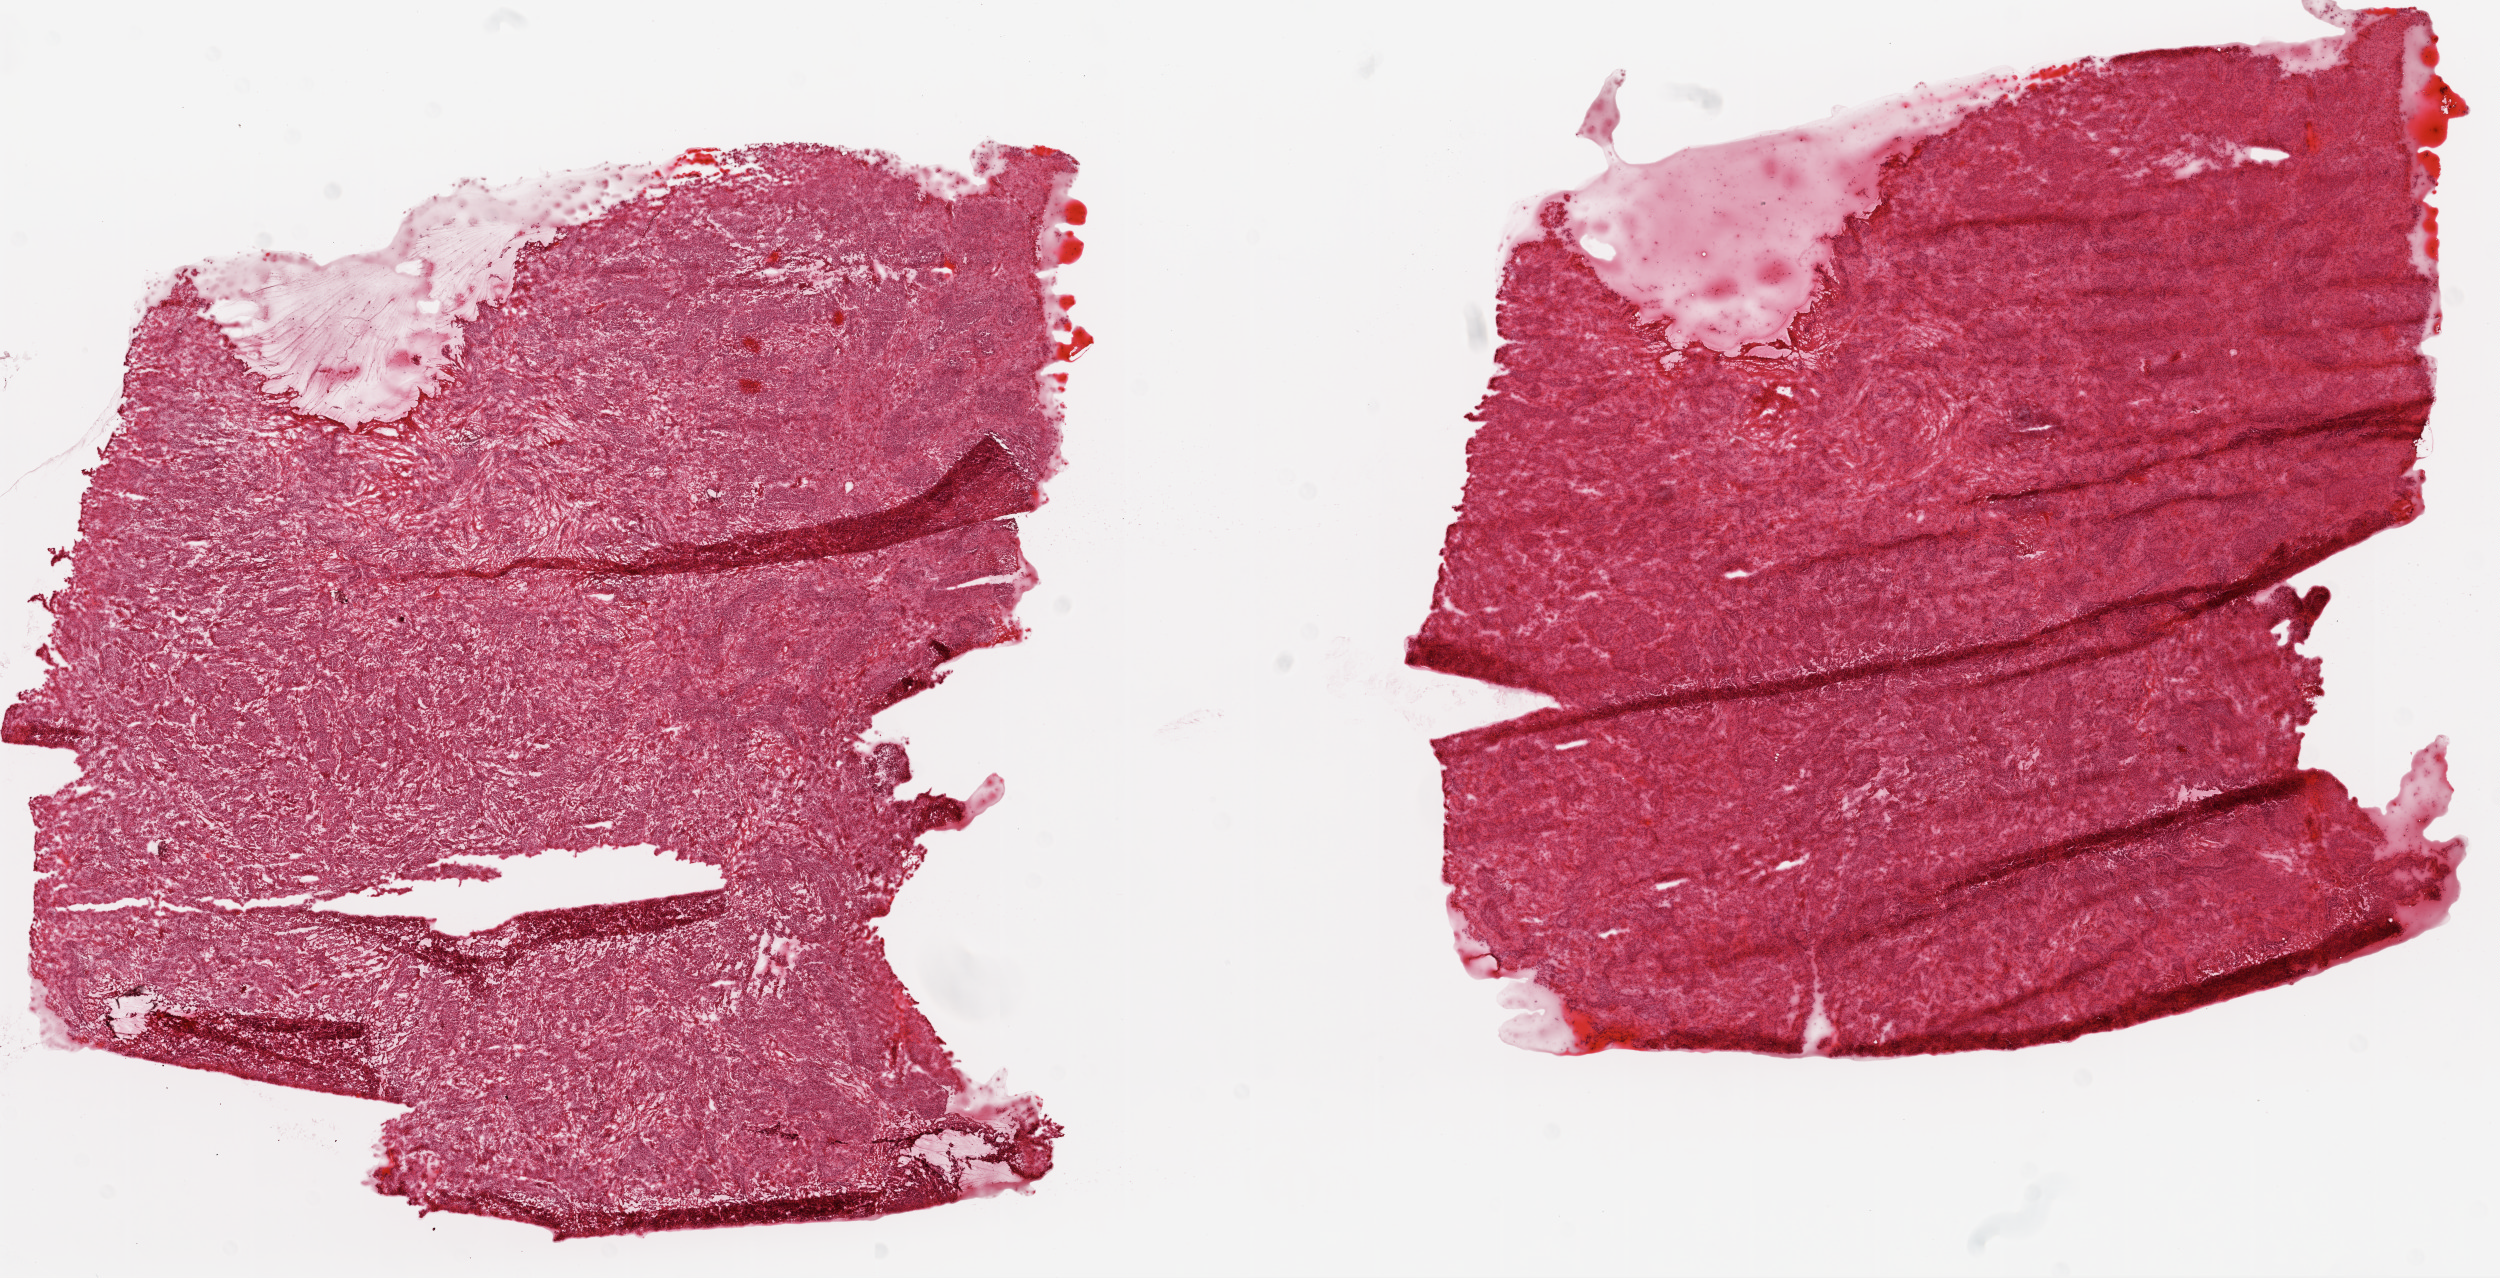
Whole-slide histology image, Hematoxylin and eosin (H&E) stained, low-resolution overview of the scanned area, about 20.1 x 10.3 mm (slide scanned at 20x), frozen section from the top of the tissue portion, ovary, primary tumour sample. Female patient; age at initial diagnosis 67 years. Histologic grade: G3 (poorly differentiated). Composition of this section per pathologist review: tumour cells 79%, tumour nuclei 80%, normal cells 0%, stromal cells 20%, necrosis 1%.
Laterality: bilateral. Histologic diagnosis: Serous cystadenocarcinoma, NOS. FIGO stage: IIIC.